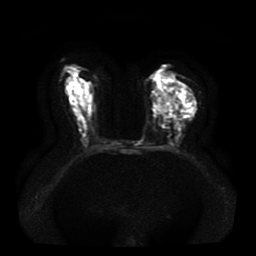
Breast MRI, one axial slice. Slice 21 of 41 in the series (ordered by position). Diffusion-weighted series; image 2 of 4 stored at this slice position (different b-values; order by instance number). 1.5 T. 5 mm slice thickness. 256 × 256 image matrix, field of view 330 × 330 mm. Female patient.
Structures marked on this image (expert manual segmentation):
- tumour on diffusion-weighted imaging: box from (x=158, y=96) to (x=178, y=112) px